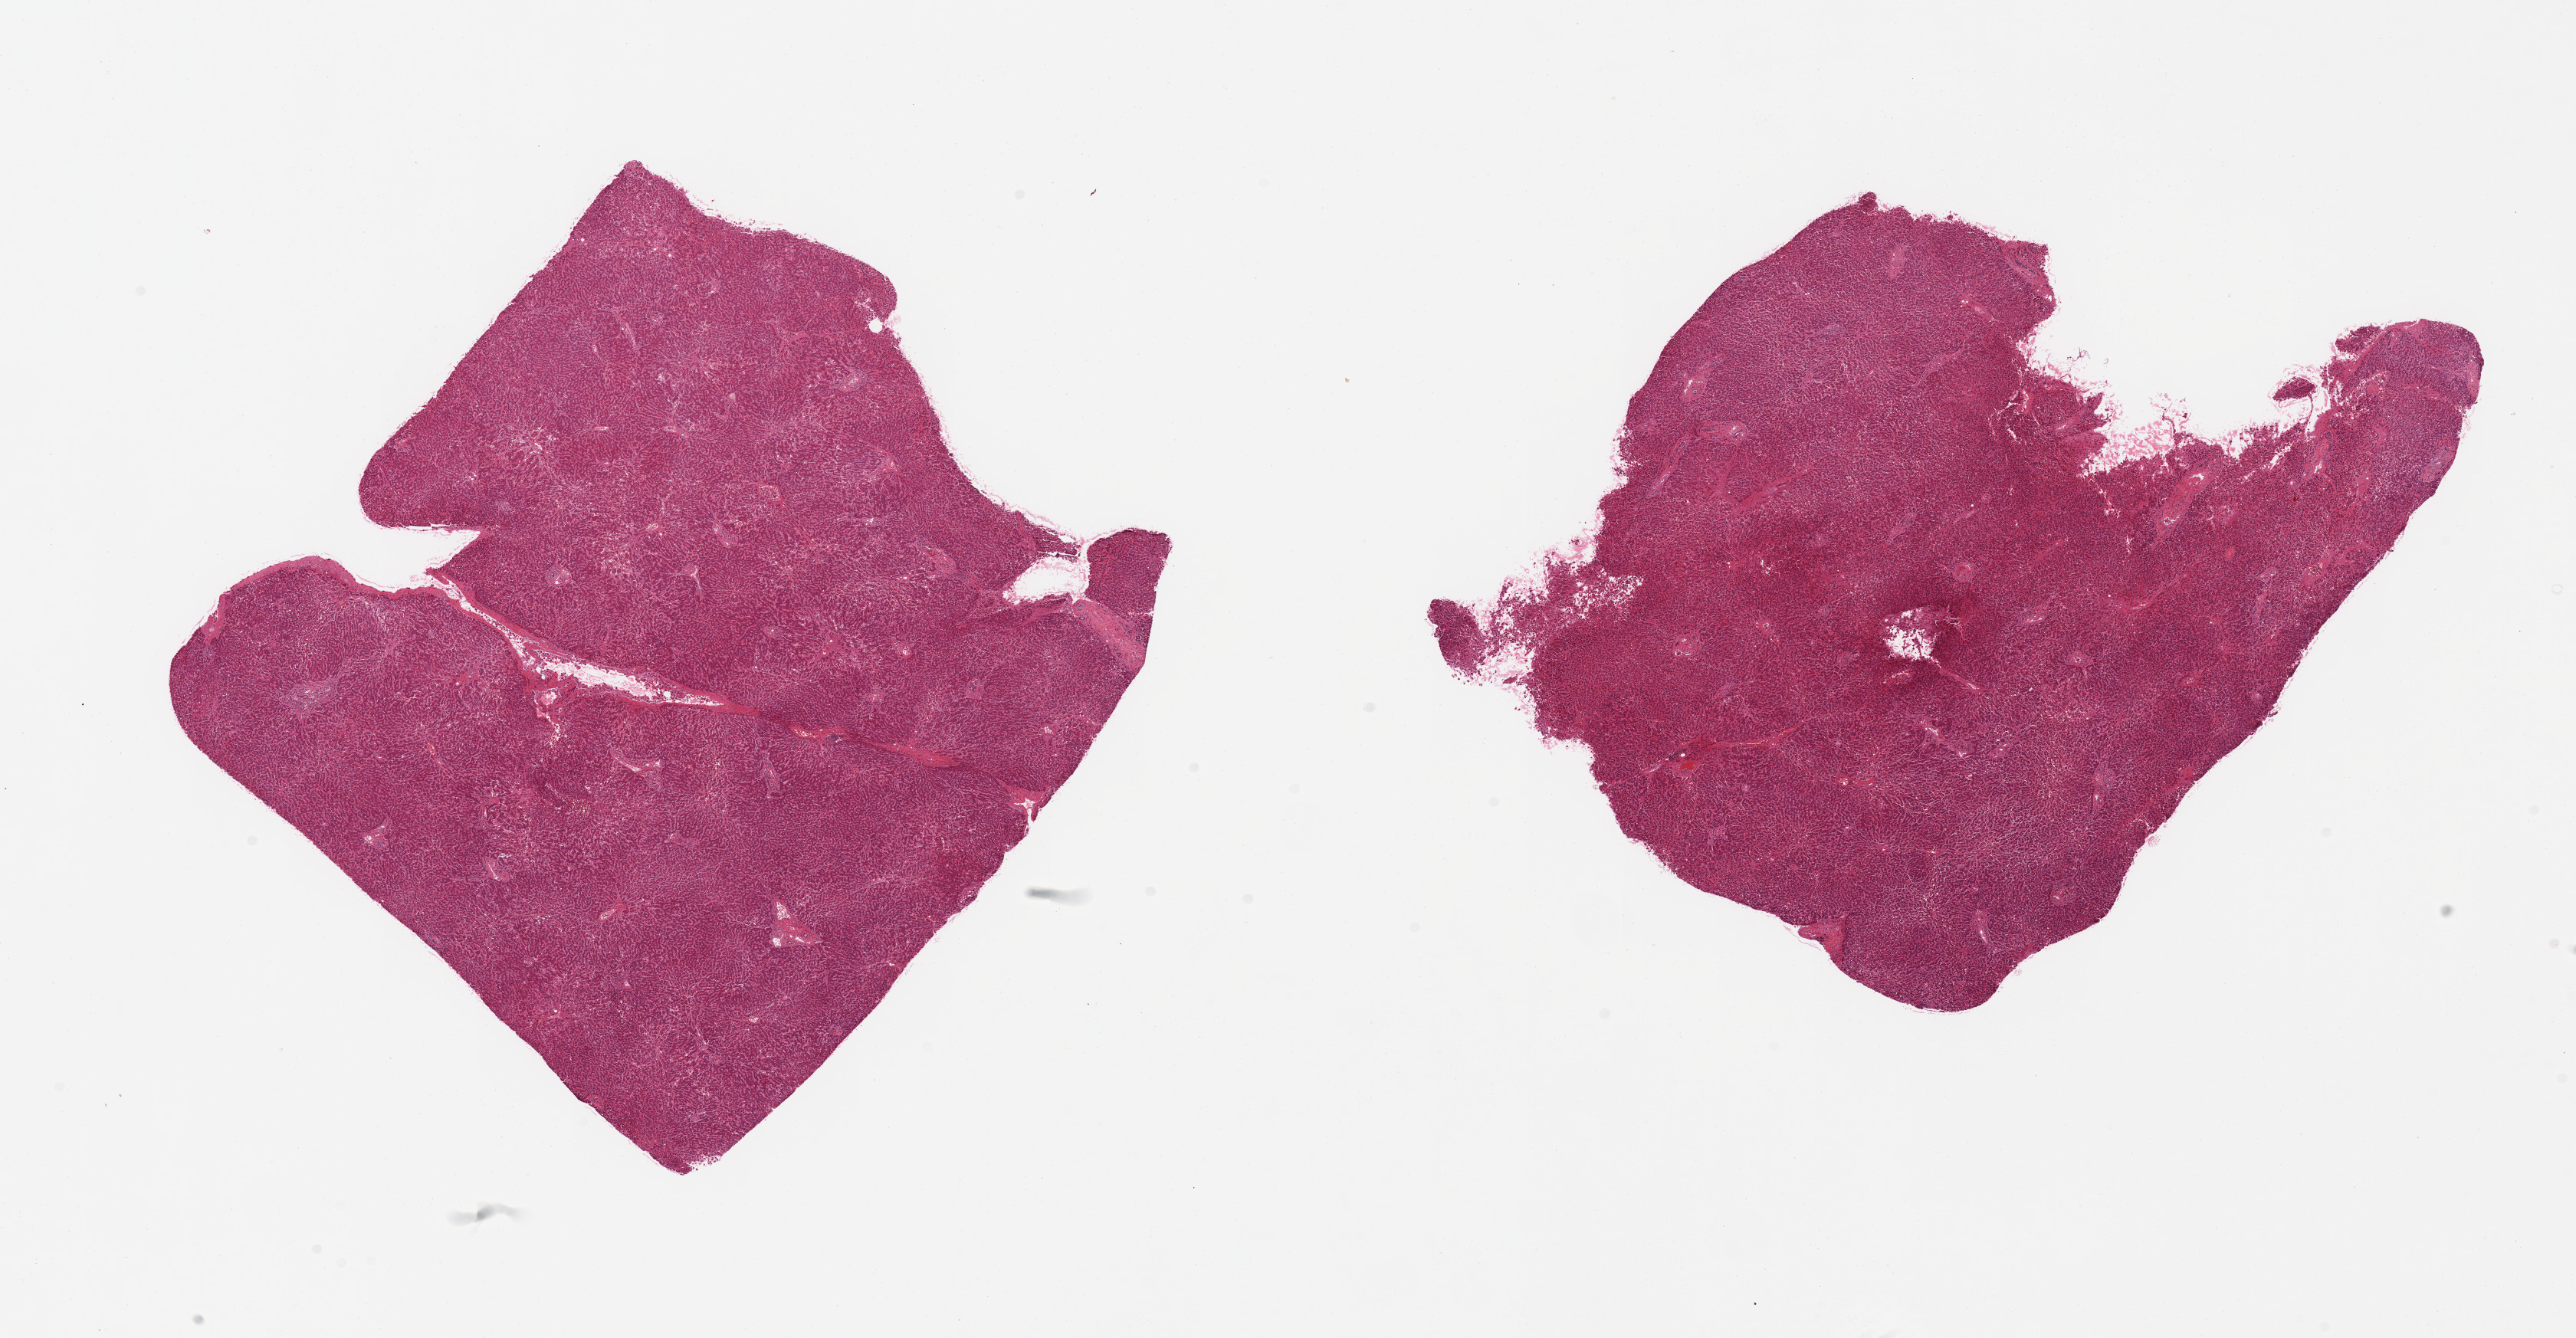
Hematoxylin and eosin (H&E) whole-slide image, brightfield — a low-resolution overview of the entire scanned area, about 26.6 x 13.8 mm (slide scanned at 20x), PAXgene-fixed paraffin-embedded (PFPE) section, sampled site (target tissue): liver, tissue donor sample. Donor sex: female.
• reviewer comment on this tissue sample: 2 pieces moderate congestion, ~10% microvesicular steatosis